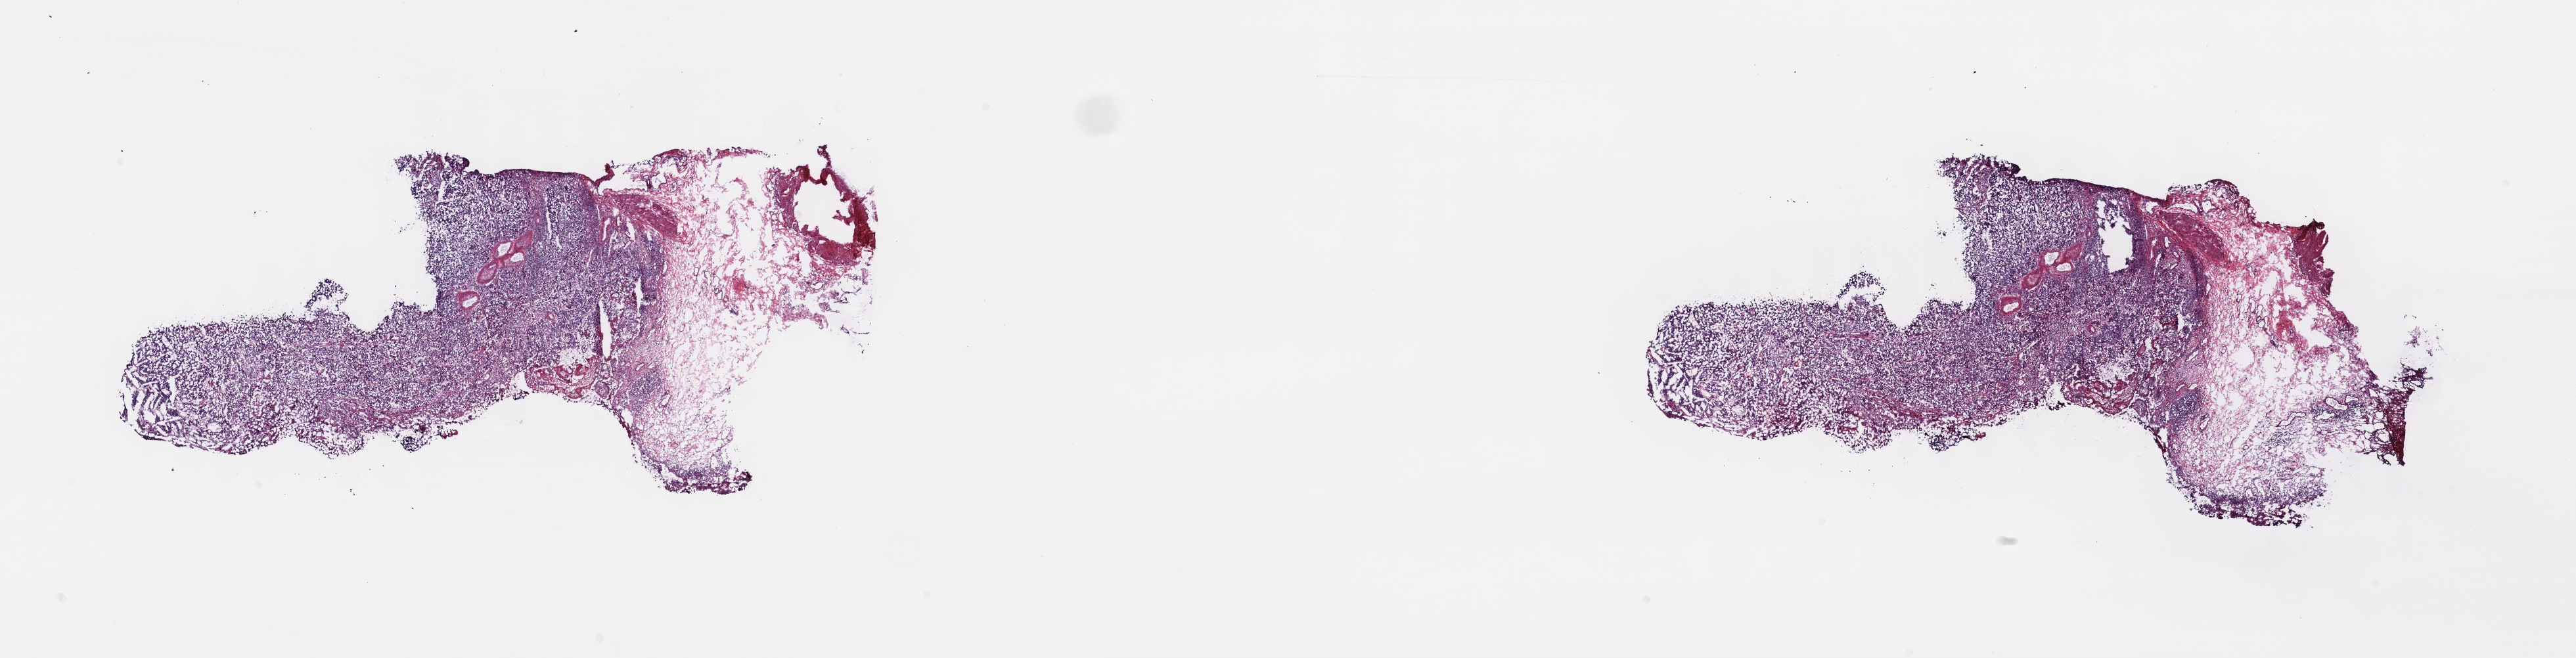
H&E-stained whole-slide image, a low-resolution overview of the entire scanned area, about 31.7 x 8.1 mm; frozen section from the top of the tissue portion; bladder, primary tumour sample. Male, age 65 years at initial diagnosis. Histologic grade: high grade. Composition of this section per pathologist review: tumour cells 75%, tumour nuclei 90%, normal cells 0%, stromal cells 25%, necrosis 0%. Infiltration values recorded for this section: lymphocyte infiltration 0%, monocyte infiltration 0%, neutrophil infiltration 0%.
Histologic diagnosis: Transitional cell carcinoma (posterior wall of bladder). AJCC pathologic stage: IV (7th edition). Lymph nodes positive (case pathology): 0 of 13 examined.